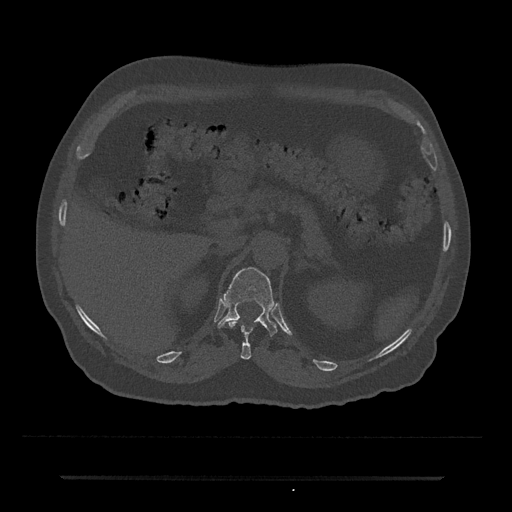
CT including the spine, one axial slice. Slice 144 of 797 in the series (ordered by position). 120 kVp. Bone window (W 1800 / L 400 HU). 0.5 mm slice thickness. 512 × 512 image matrix, field of view 437 × 437 mm. Patient: male, 69 years. From the clinical record (not read from this slice): primary cancer: prostate.
Outlined on this slice (semi-automatic segmentation, software-assisted and operator-edited):
- T11 vertebra: bounding box (x1, y1, x2, y2) in pixels: (228, 321, 253, 360)
- T12 vertebra: (217, 267, 277, 336)